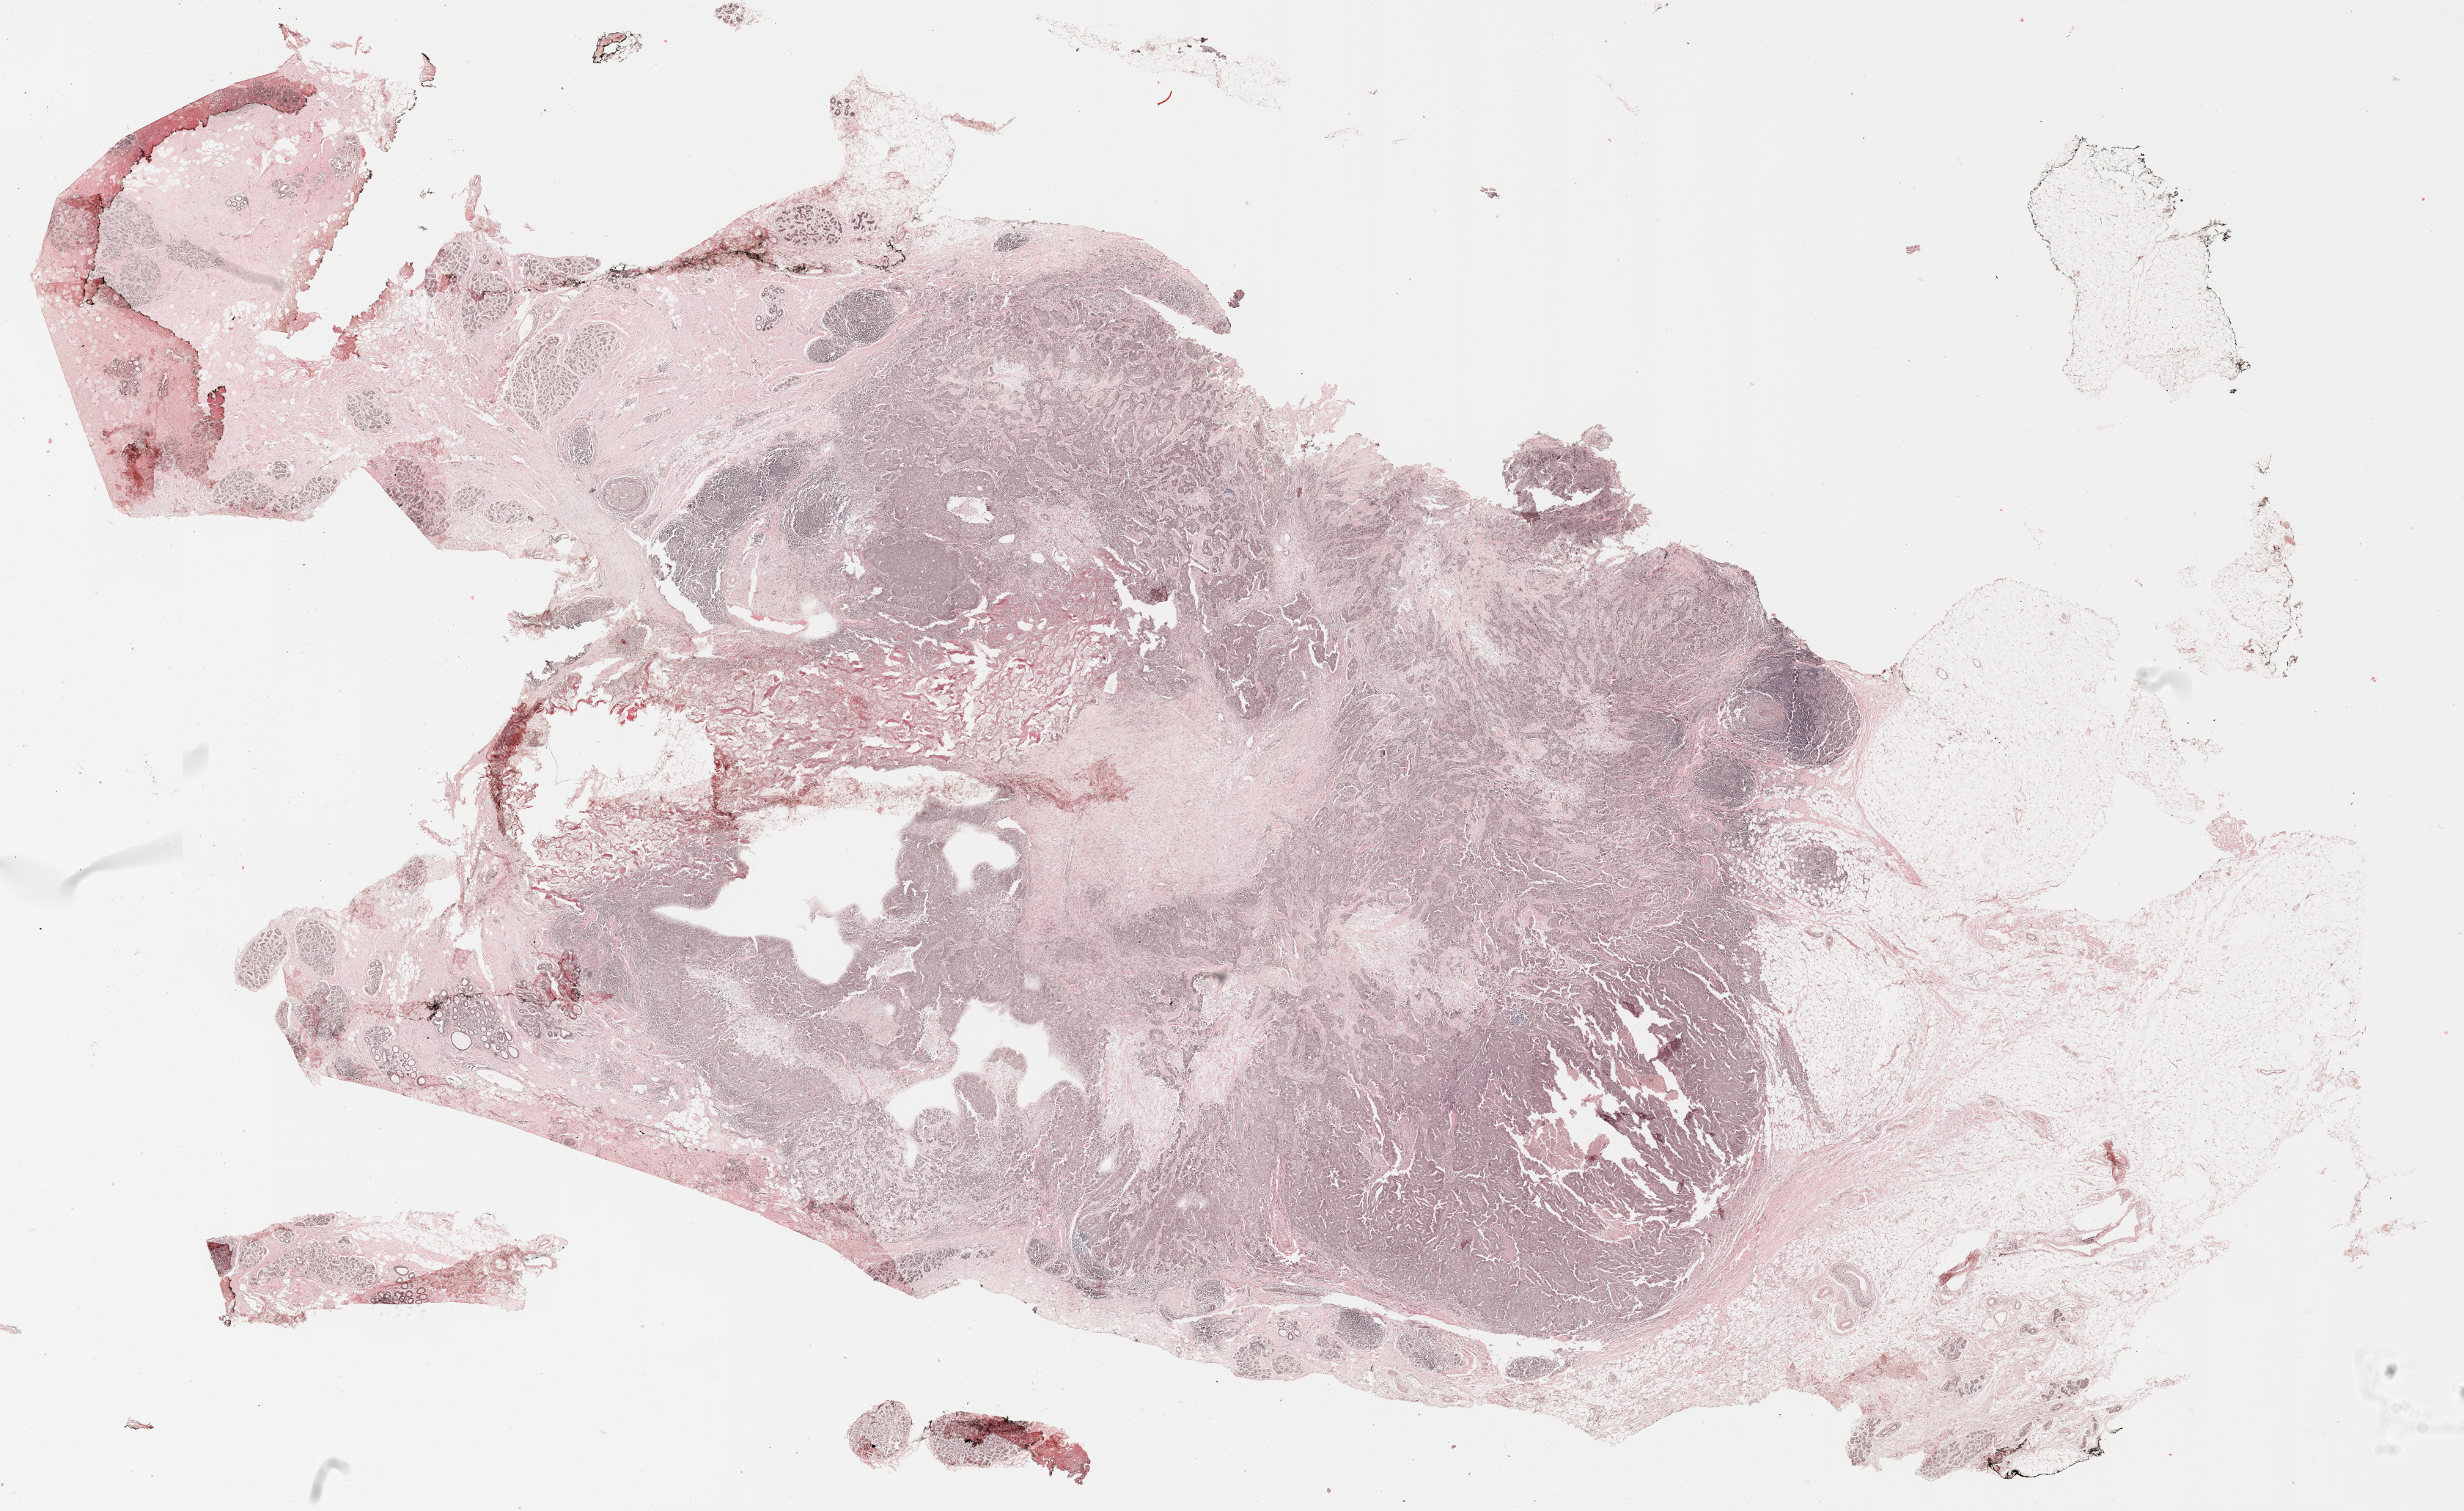
Digitized H&E-stained tissue section (whole slide), a low-resolution overview of the entire scanned area, about 26.8 x 16.5 mm; formalin-fixed paraffin-embedded (FFPE) diagnostic section; primary tumour sample from the breast. Female patient; age at initial diagnosis 41 years.
Pathologic diagnosis: Infiltrating duct carcinoma, NOS.